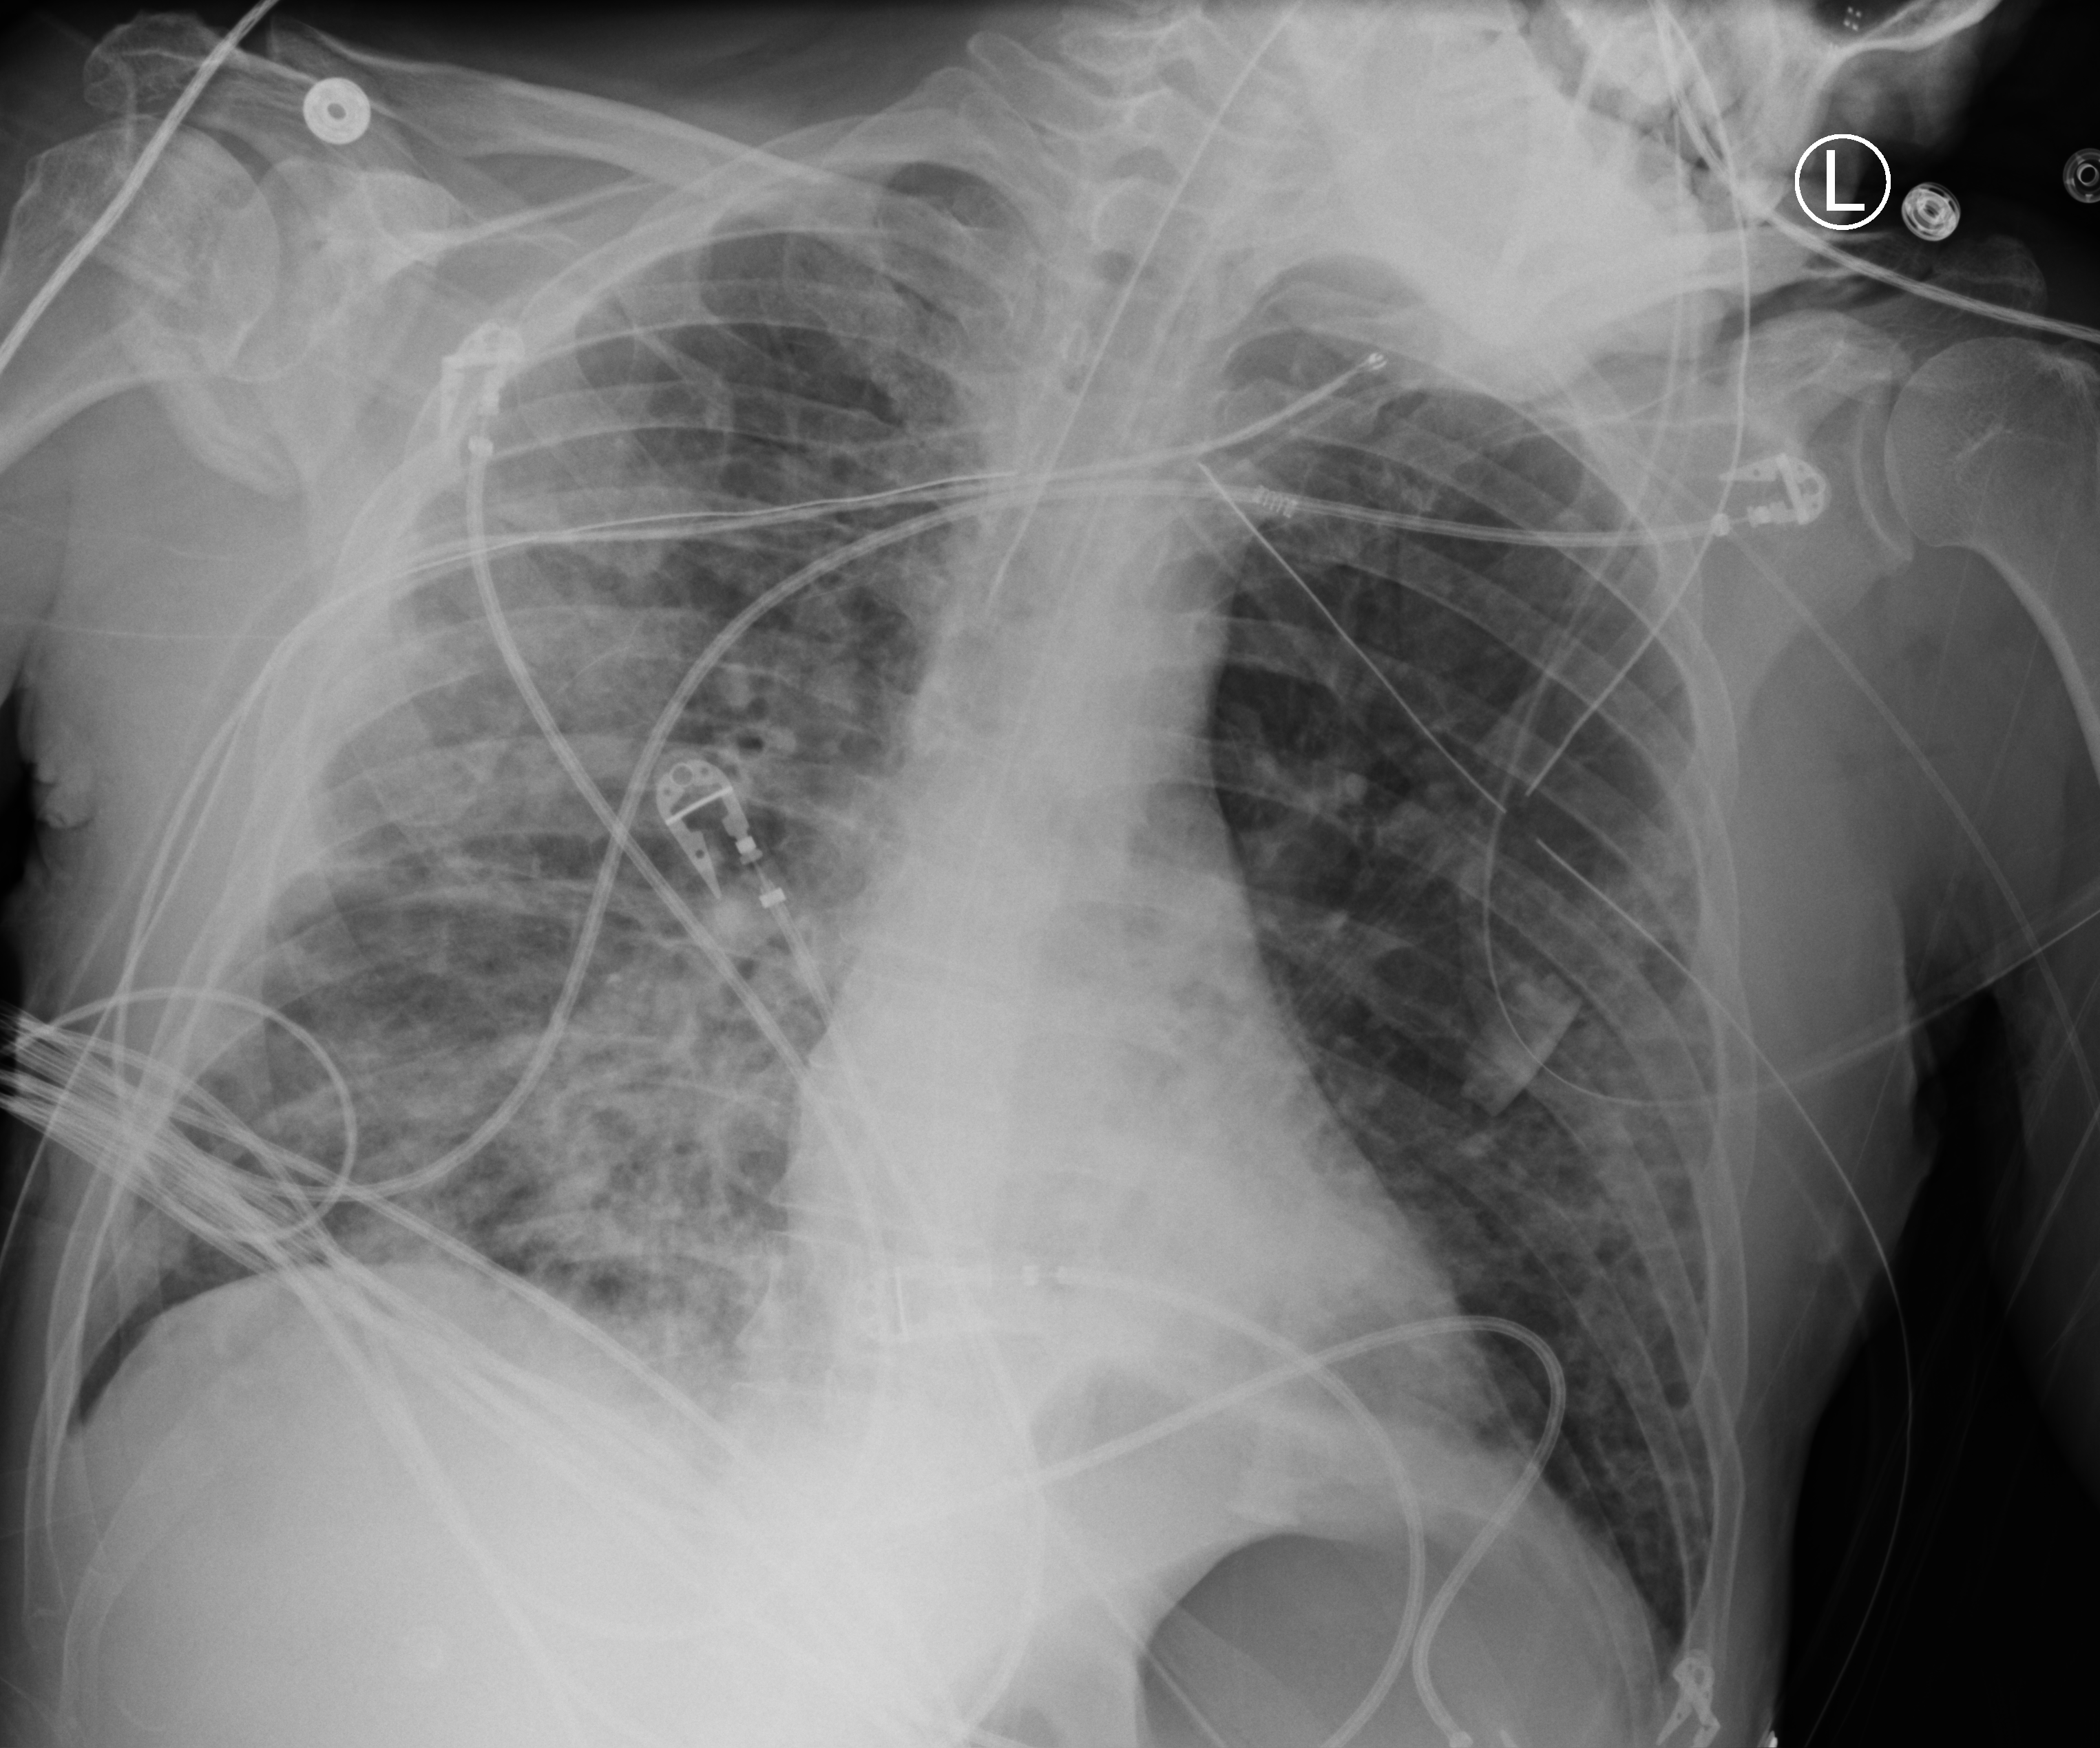
Portable chest radiograph, anteroposterior (AP) projection. Male patient hospitalised with COVID-19, age 18–59 years.
Hospital-stay facts (about this admission, not read from this image; timing relative to this image not recorded): admitted to intensive care during this hospital stay: yes.